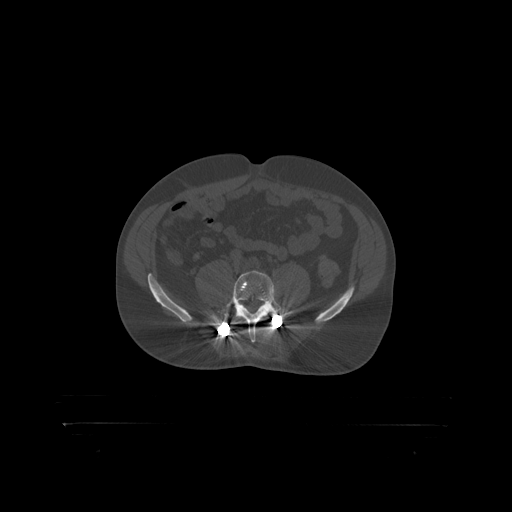
CT including the spine, one axial slice; slice 208 of 399 in the series (ordered by position); reconstruction kernel STANDARD; 120 kVp; bone window (W 1800 / L 400 HU); 1.25 mm slice thickness; 512 × 512 image matrix, field of view 650 × 650 mm. Patient: male, 46 years. Case-level facts recorded for this patient, not image findings: primary cancer: skin.
Annotated regions visible in this slice (semi-automatic segmentation, software-assisted and operator-edited):
- L5 vertebra: bounding box [x1, y1, x2, y2] px = [225, 271, 283, 319]